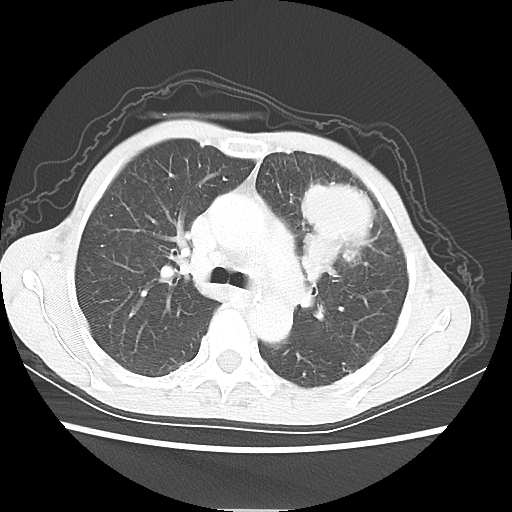
Chest CT, one axial slice. Slice 39 of 56 in the series (ordered by position). Lung window (W 1500 / L -600 HU). 5 mm slice thickness. 512 × 512 image matrix, field of view 331 × 331 mm. Female patient, age 60 years. From the clinical record (not read from this slice): clinical TNM (as recorded): T4 N1 M0.
Structures marked on this image (rectangle marked by the reading radiologist):
- lung tumour (recorded histology: adenocarcinoma): bounding box [x1, y1, x2, y2] px = [291, 171, 374, 283]